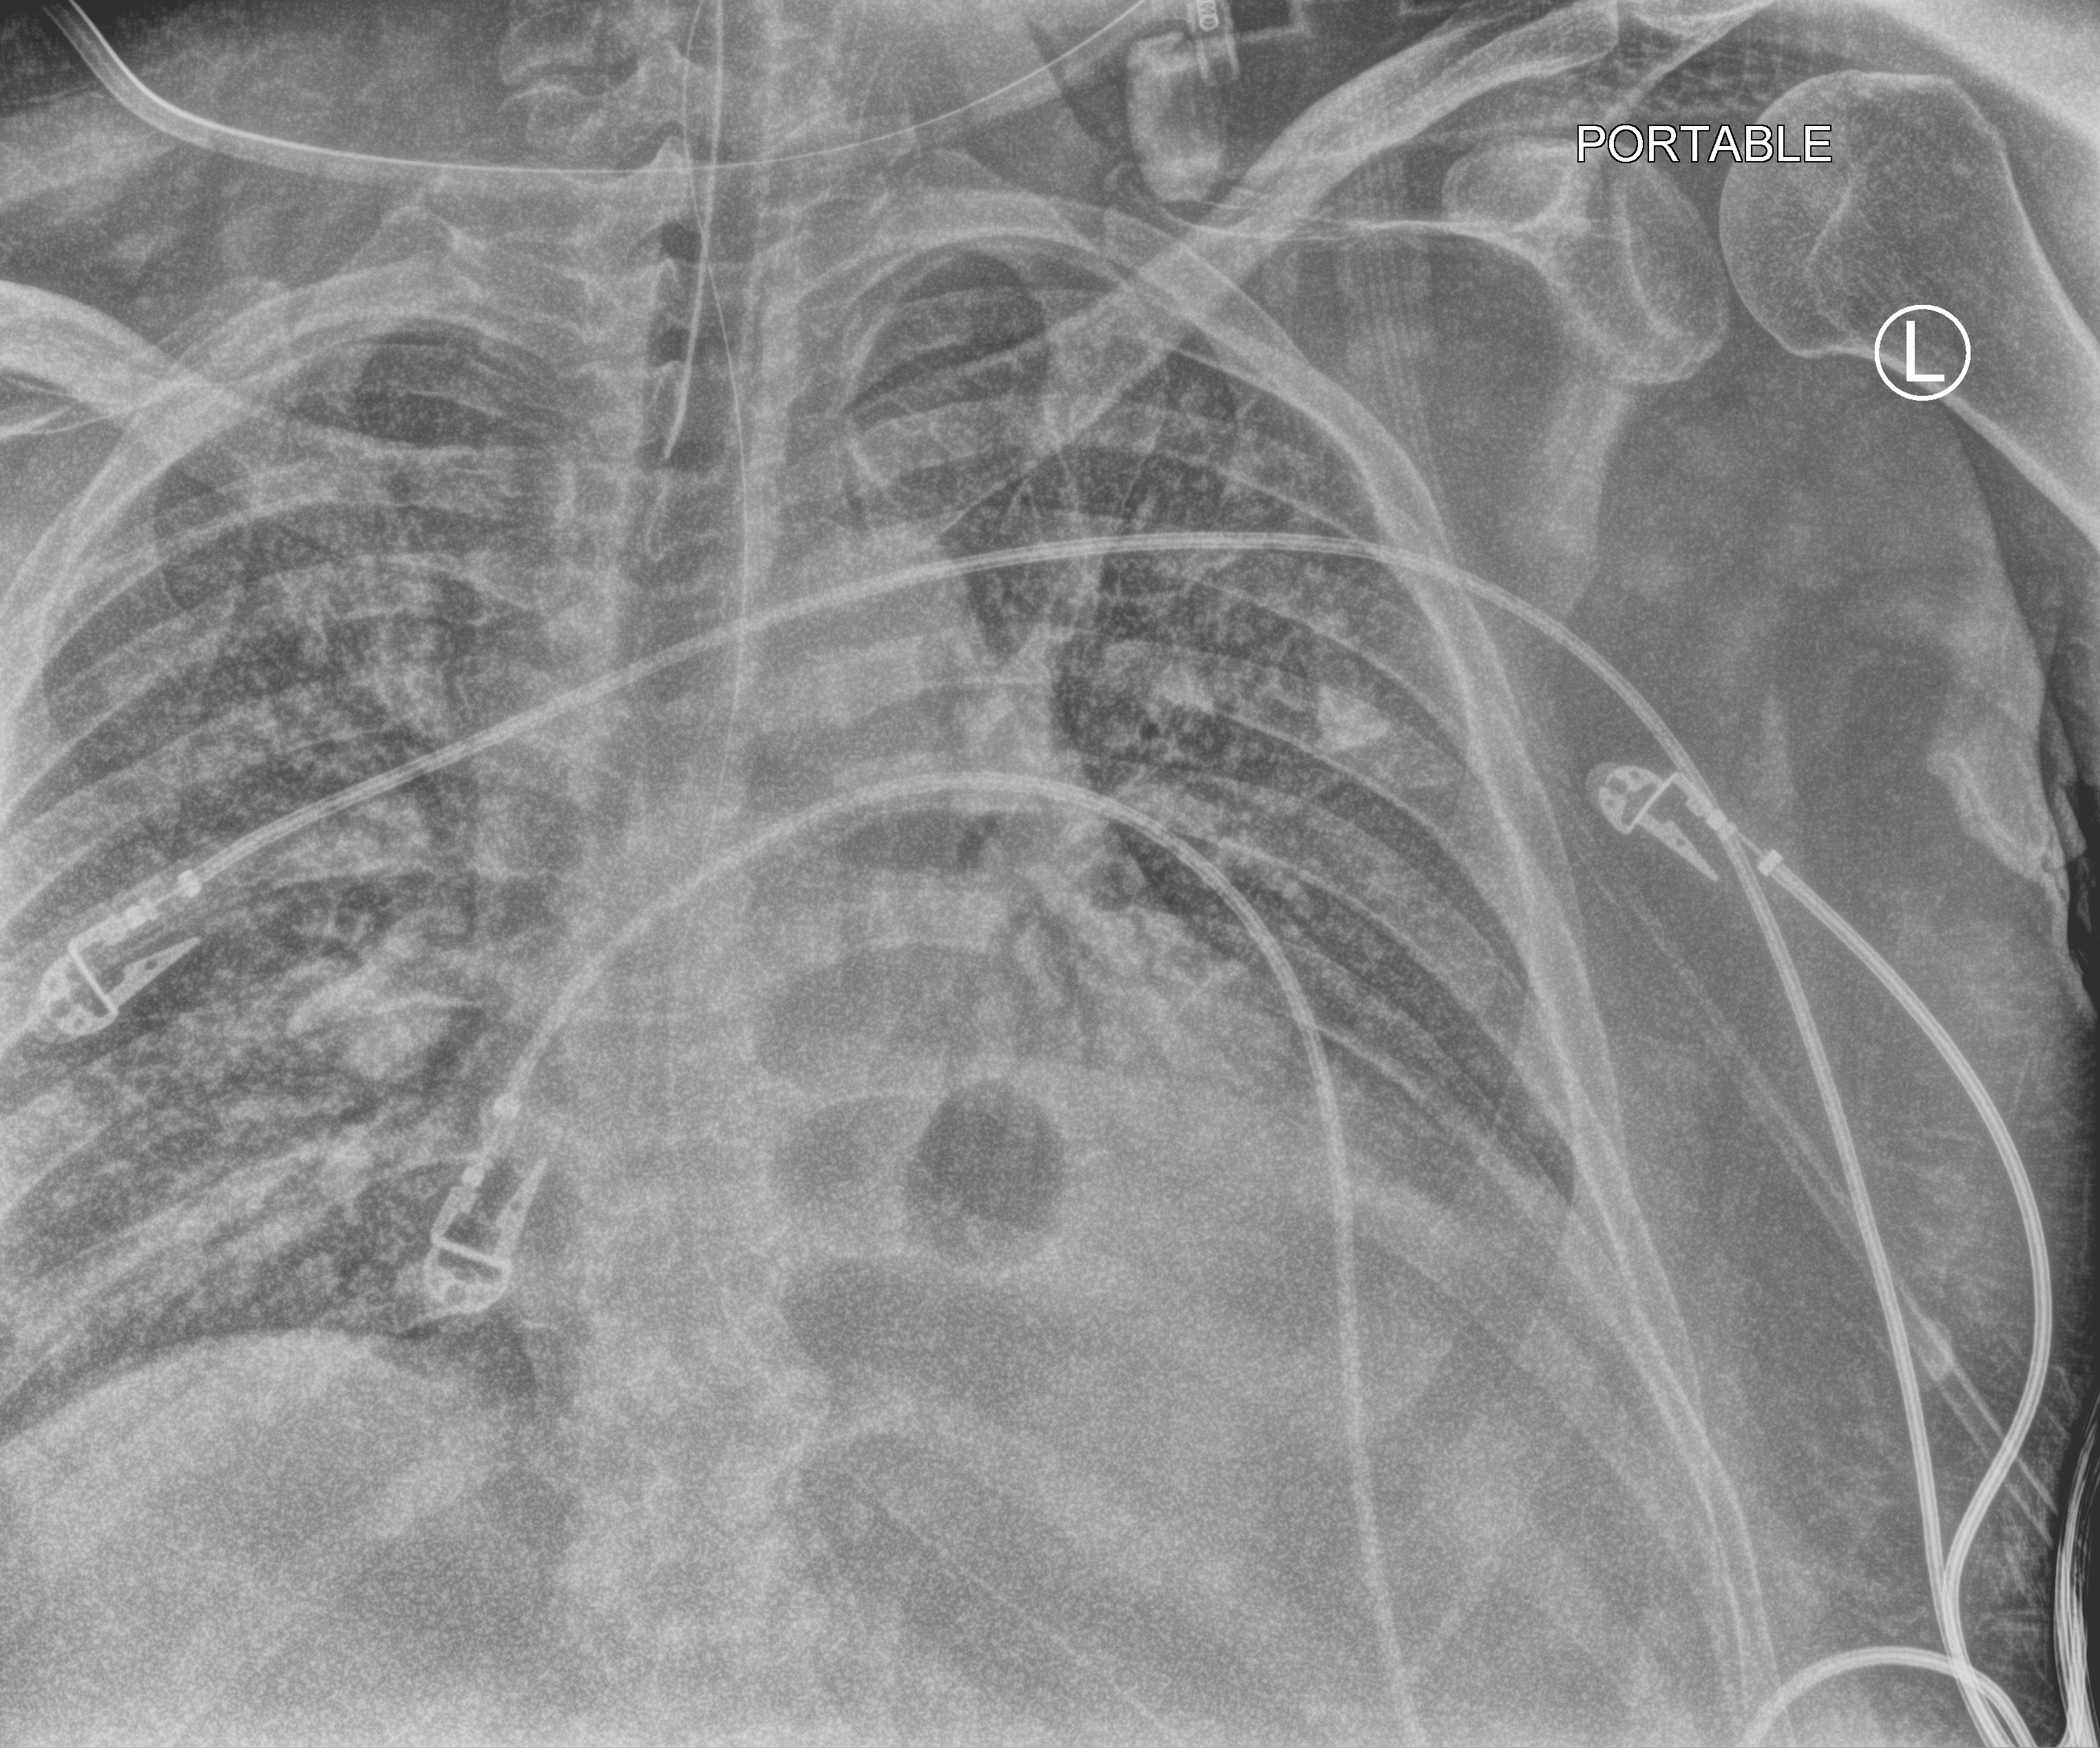
Chest X-ray (portable); anteroposterior (AP) projection. Patient hospitalised with COVID-19, aged 18–59 years.
Admission-level facts for this patient (not findings on this image; timing relative to this image not recorded): length of hospital stay: 26 days; admitted to intensive care during this hospital stay: yes.